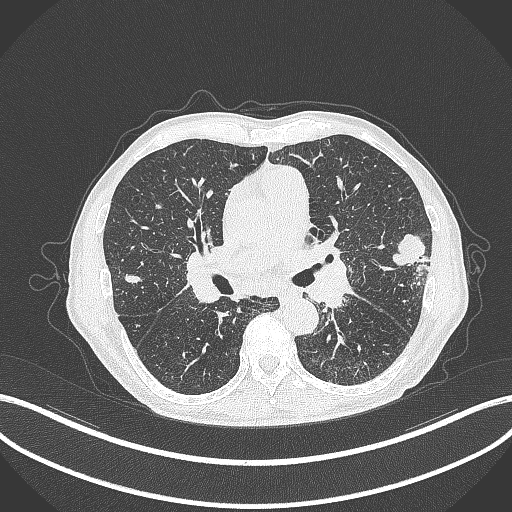
Chest CT, one axial slice; position 226 of 463 along the scan axis; lung window (W 1500 / L -600 HU); 1 mm slice thickness; 512 × 512 image matrix. Patient: male, 74 years. From the clinical record (not read from this slice): clinical TNM (as recorded): T2a N1 M0.
Annotated regions visible in this slice (bounding box drawn by a radiologist):
- lung tumour (recorded histology: adenocarcinoma): bounding box (x1, y1, x2, y2) in pixels: (390, 230, 430, 275)